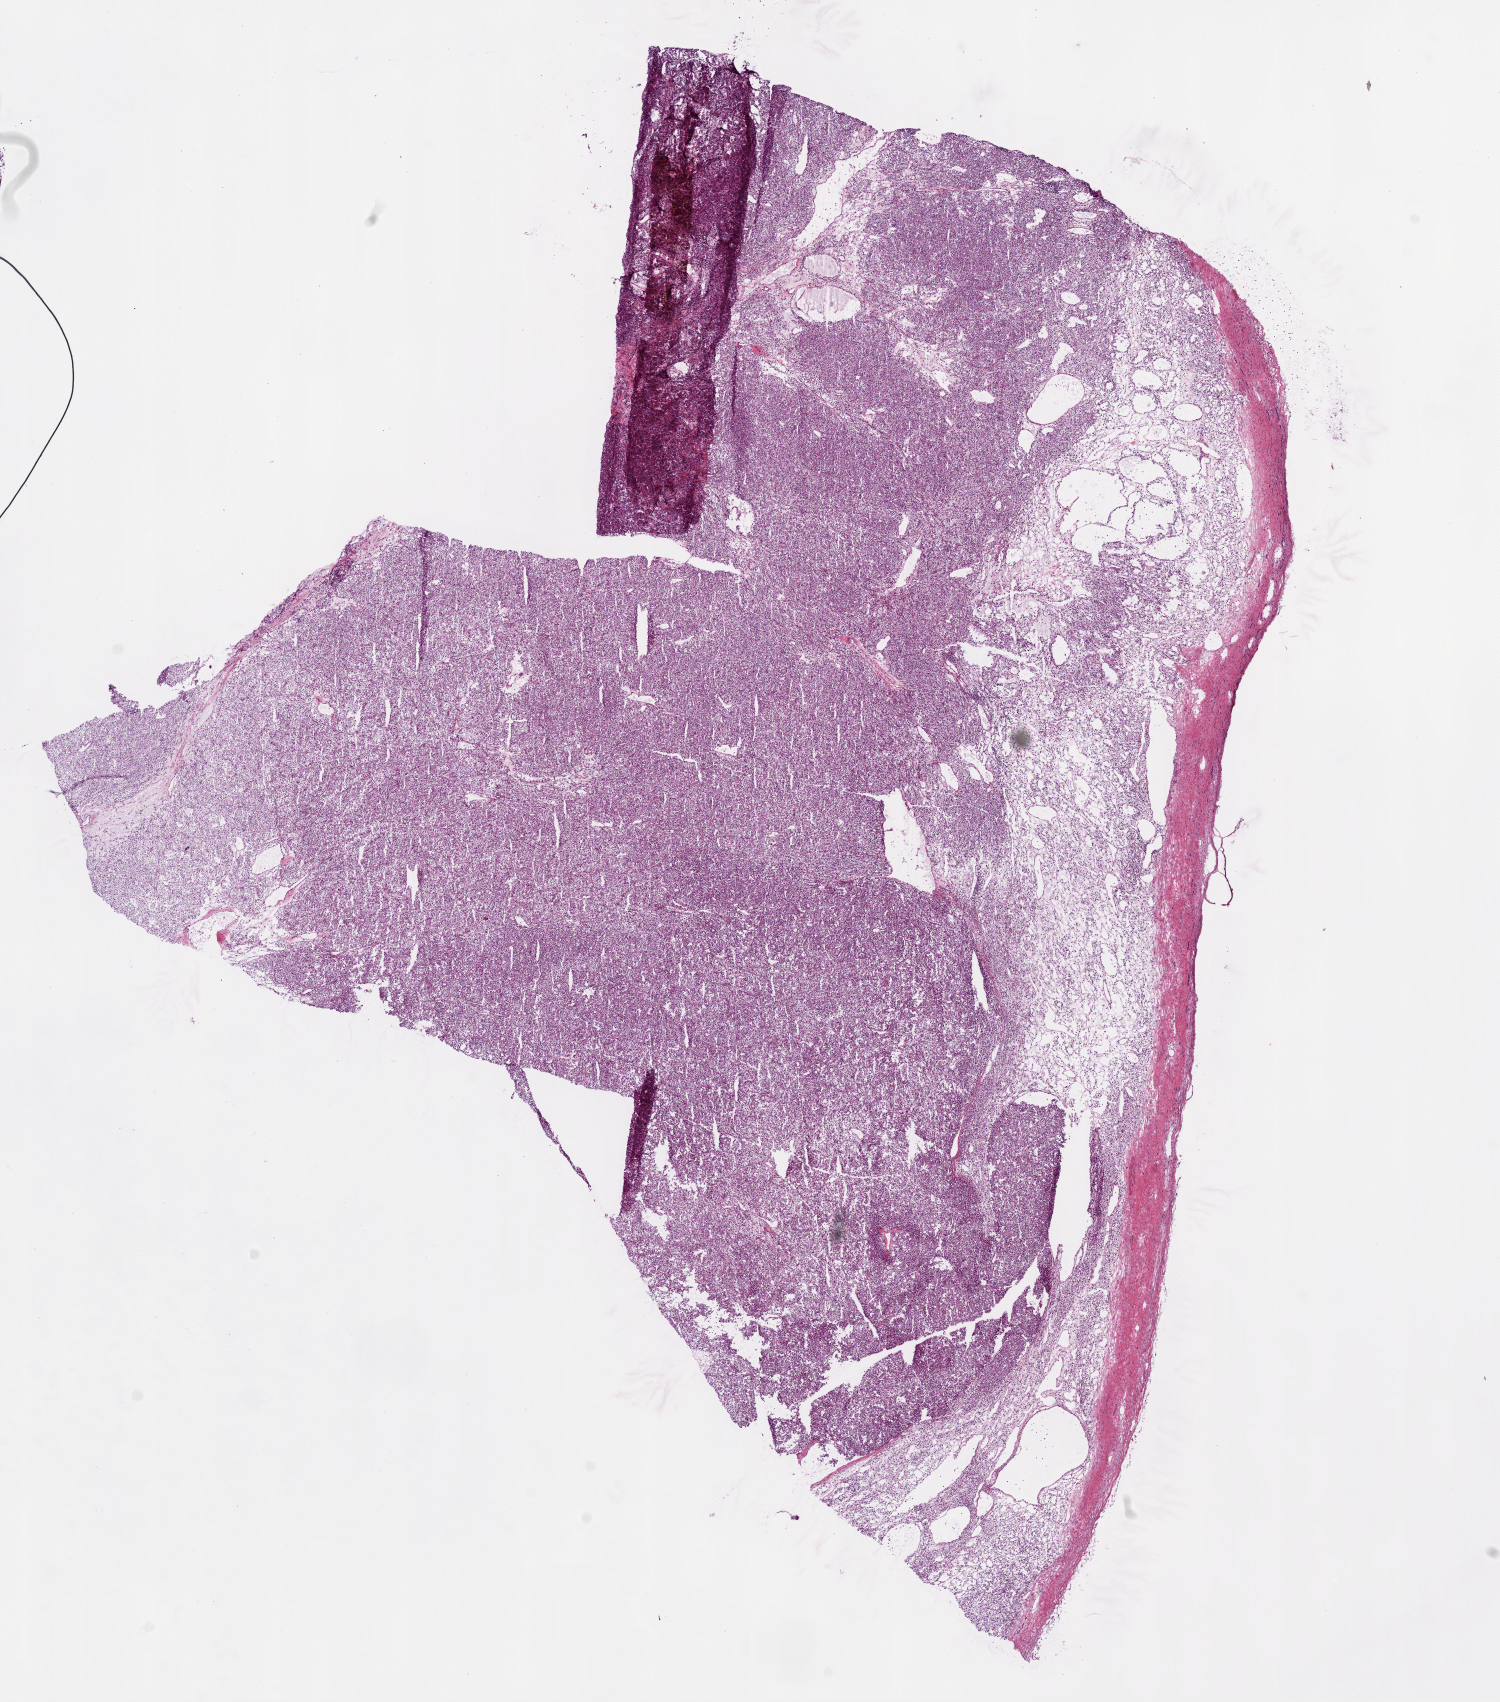
Digitized H&E-stained tissue section (whole slide) — whole scanned area (about 12.0 x 13.7 mm) shown as a low-resolution overview, frozen section from the bottom of the tissue portion, sample: primary tumour, kidney. Female, age 68 years at initial diagnosis. Histologic grade: G3 (poorly differentiated). Pathologist review of this section (percent, as recorded): tumour cells 95%, tumour nuclei 95%, normal cells 0%, stromal cells 5%, necrosis 0%. Inflammatory infiltration, as recorded: lymphocyte infiltration 1%, monocyte infiltration 0%, neutrophil infiltration 0%.
- TNM: T3 N0 M1
- pathologic diagnosis: Clear cell adenocarcinoma, NOS
- laterality: right
- AJCC pathologic stage: IV (7th edition)